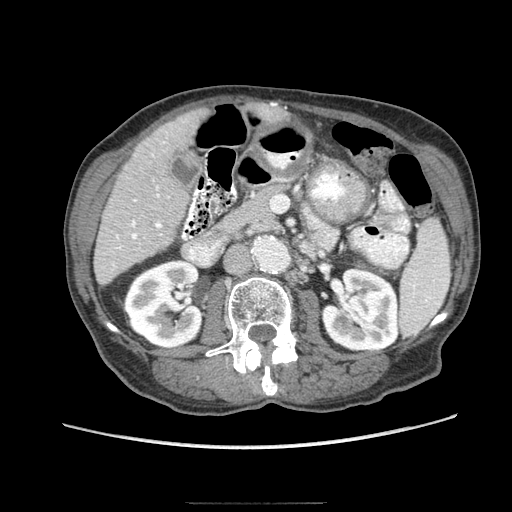
Contrast-enhanced abdominal CT (liver protocol), one axial slice. Position 31 of 83 along the scan axis. Reconstruction kernel STANDARD. 140 kVp. Soft-tissue window (W 400 / L 40 HU). 2.5 mm slice thickness. 512 × 512 image matrix. From the clinical record (not read from this slice): diagnosis: hepatocellular carcinoma (patient treated with transarterial chemoembolisation; whether this scan precedes or follows treatment is not stated here); TNM stage (as recorded): Stage-I; Child-Pugh class: A; tumour nodularity: uninodular.
Structures marked on this image (semi-automatically segmented with operator editing):
- liver parenchyma outside the tumour (the mass and vessels are separate outlines, so this box may not span the whole liver): bounding box [x1, y1, x2, y2] px = [94, 108, 208, 284]
- liver vessels: [113, 142, 165, 266]